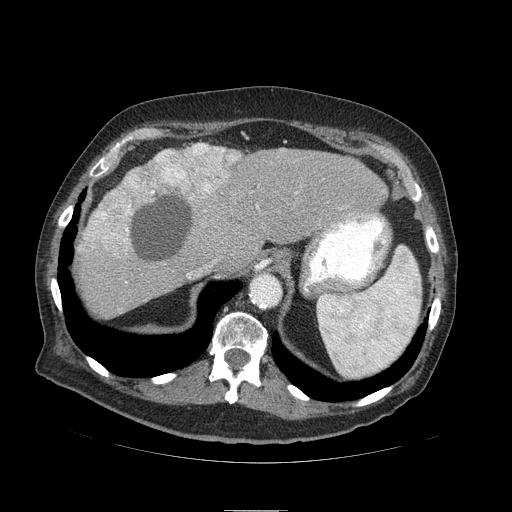
Contrast-enhanced abdominal CT (liver protocol), one axial slice. Reconstruction kernel STANDARD. Soft-tissue window (W 400 / L 40 HU). 512 × 512 image matrix, field of view 440 × 440 mm. Case-level facts recorded for this patient, not image findings: diagnosis: hepatocellular carcinoma (patient treated with transarterial chemoembolisation; whether this scan precedes or follows treatment is not stated here); TNM stage (as recorded): Stage-IIIA; Child-Pugh class: B; tumour differentiation: well differentiated.
Outlined on this slice (semi-automatic segmentation, software-assisted and operator-edited):
- liver parenchyma outside the tumour (the mass and vessels are separate outlines, so this box may not span the whole liver): bounding box (x1, y1, x2, y2) in pixels: (76, 142, 387, 316)
- mass: (83, 144, 241, 262)